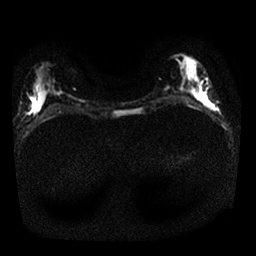
Breast MRI, one axial slice. Slice 8 of 25 in the series (ordered by position). Diffusion-weighted series; image 2 of 4 stored at this slice position (different b-values; order by instance number). 1.5 T. 4 mm slice thickness. 256 × 256 image matrix, field of view 320 × 320 mm. Female patient.
Annotated regions visible in this slice (manually delineated by an expert):
- tumour on diffusion-weighted imaging: bounding box (x1, y1, x2, y2) in pixels: (202, 96, 206, 99)